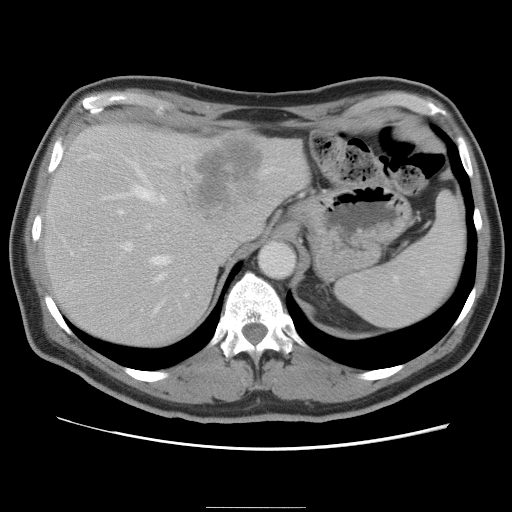
Contrast-enhanced abdominal CT, one axial slice; slice 60 of 87 in the series (ordered by position); 120 kVp; soft-tissue window (W 400 / L 40 HU); 5 mm slice thickness; 512 × 512 image matrix, field of view 363 × 363 mm. Male patient, age 63 years. From the clinical record (not read from this slice): diagnosis: colorectal cancer liver metastases, imaged before liver resection; multiple liver metastases: no.
Structures marked on this image (manually delineated by an expert):
- hepatic veins: bounding box (x1, y1, x2, y2) in pixels: (101, 159, 186, 314)
- liver: (43, 122, 310, 348)
- planned liver remnant (the part of the liver to remain after resection): (43, 156, 218, 348)
- portal vein (with intrahepatic branches): (117, 209, 189, 297)
- liver metastasis: (198, 138, 263, 206)